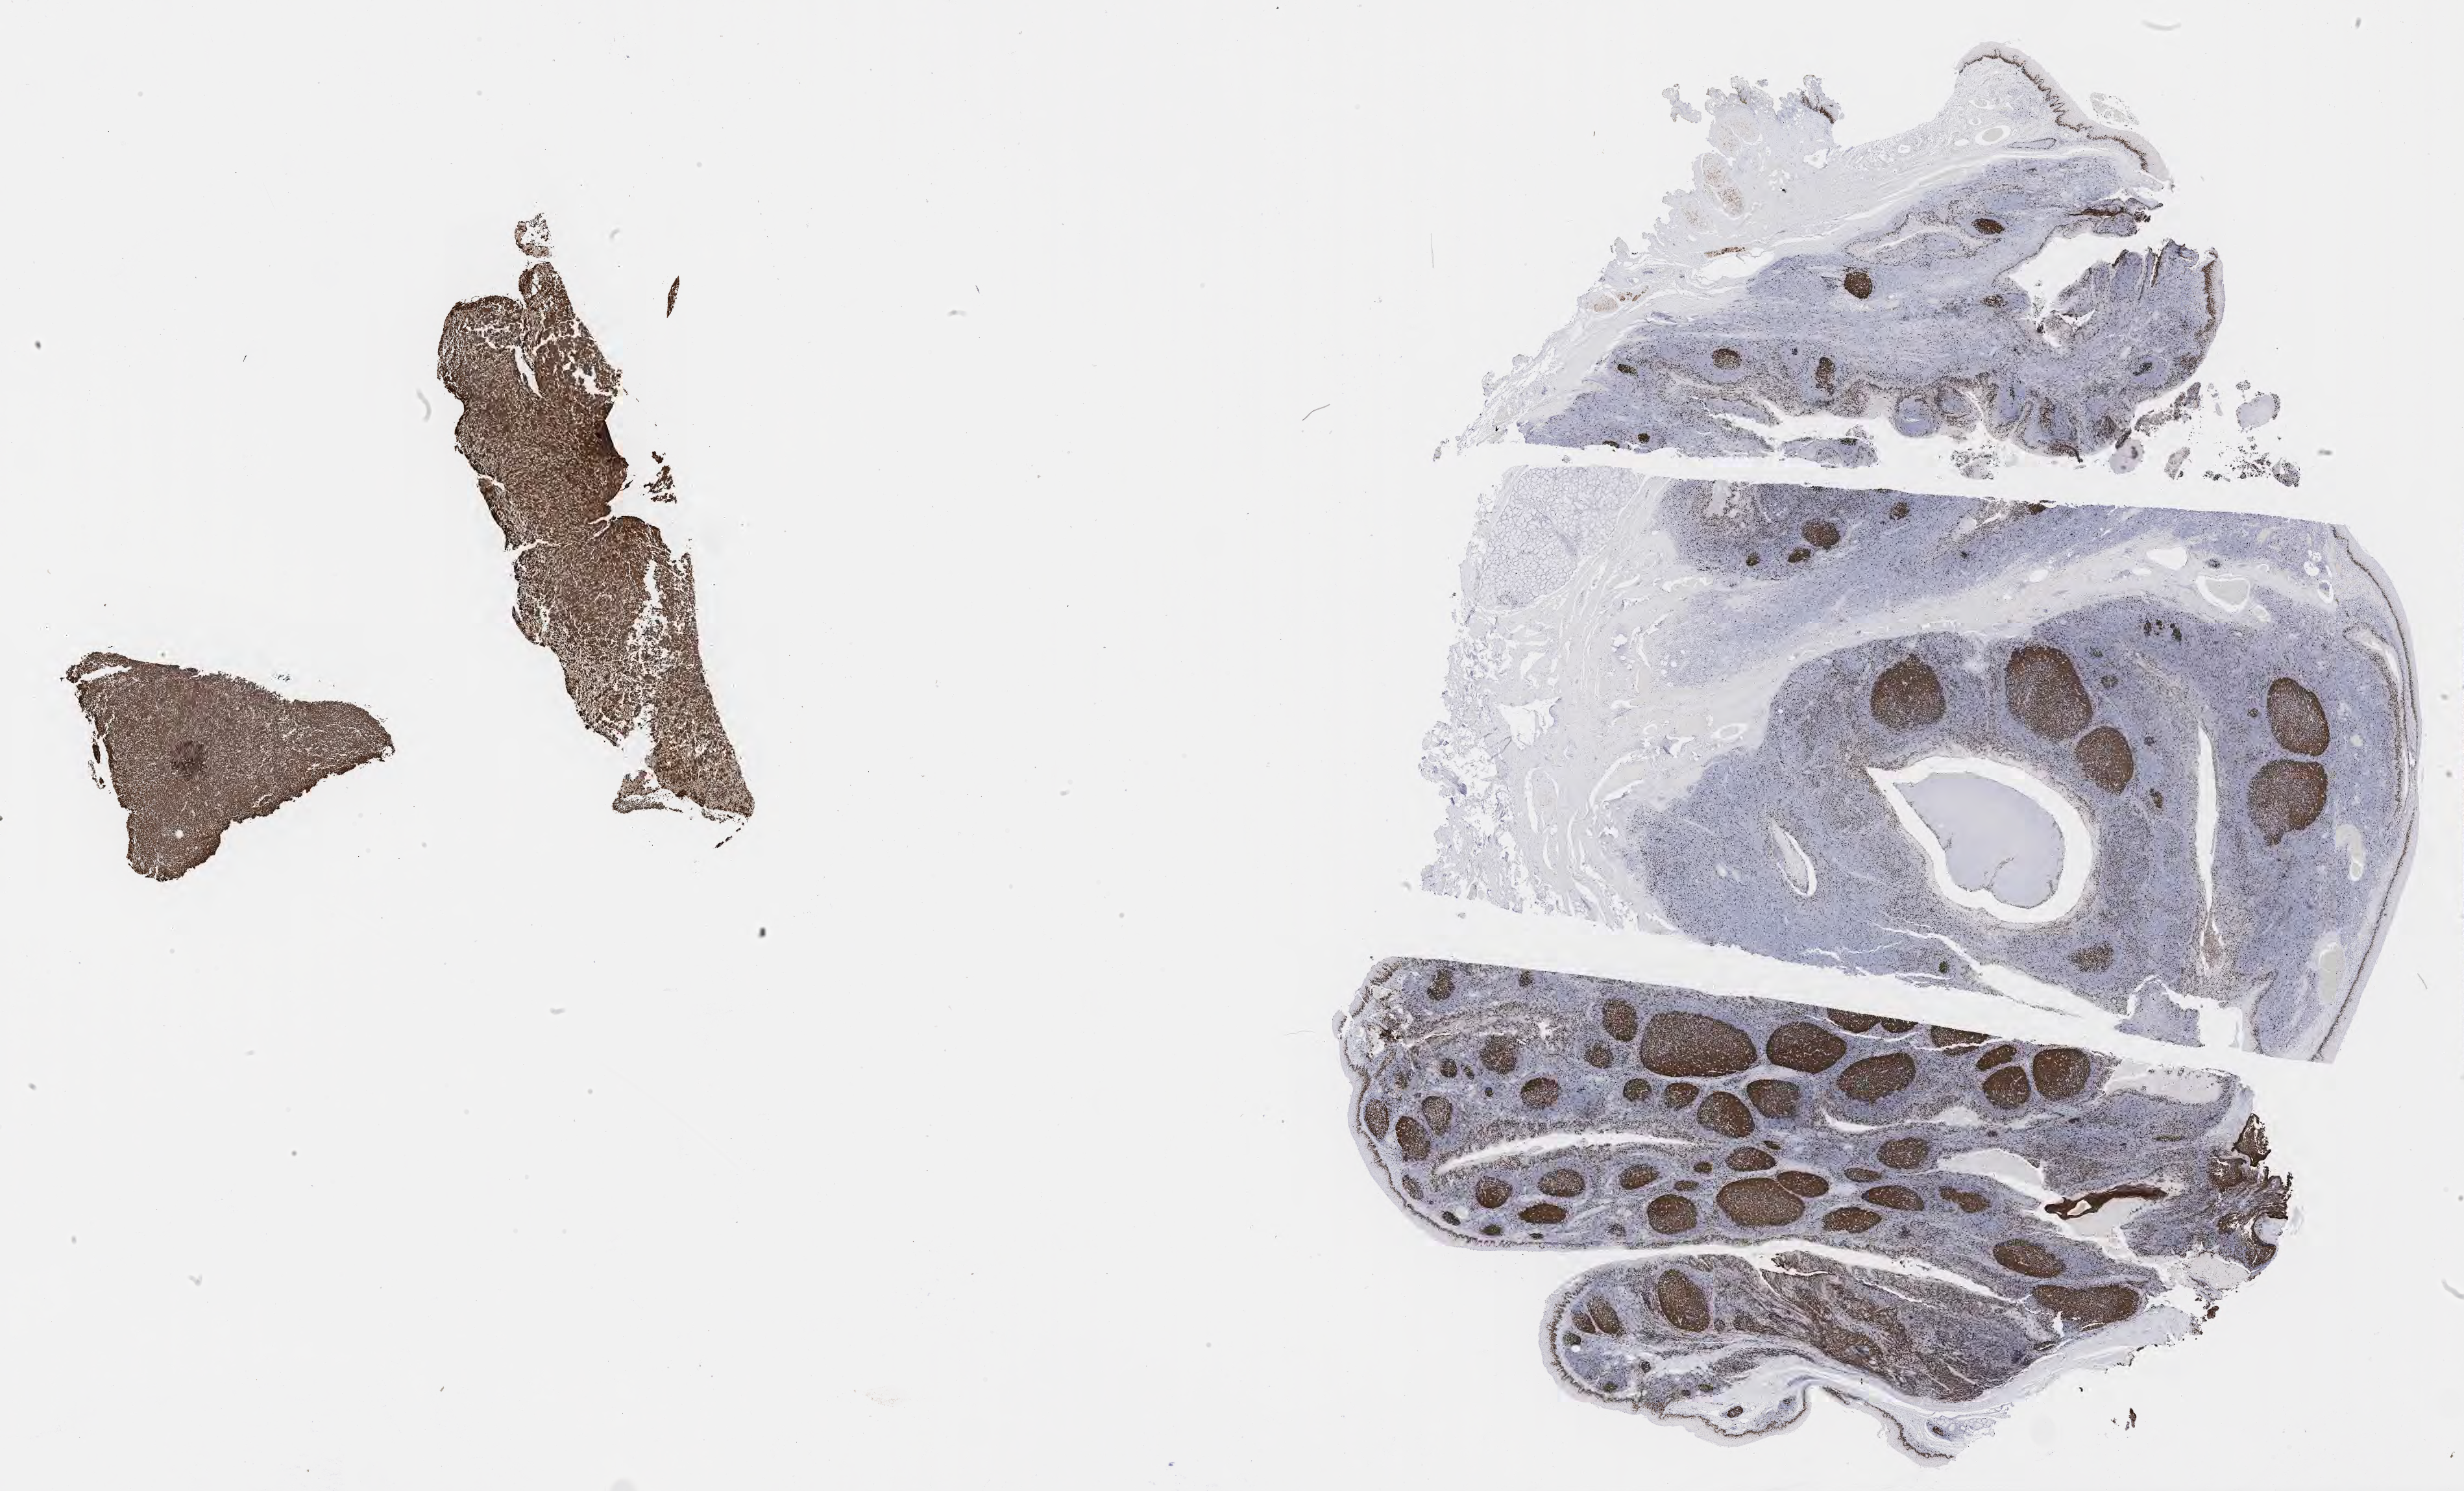
Immunohistochemistry (IHC) whole-slide image stained for Ki-67 — whole scanned area (about 30.7 x 18.6 mm) shown as a low-resolution overview. Specimen: tumor tissue. Patient: male, age at initial diagnosis 2 years.
Diagnosis: Burkitt lymphoma, NOS.